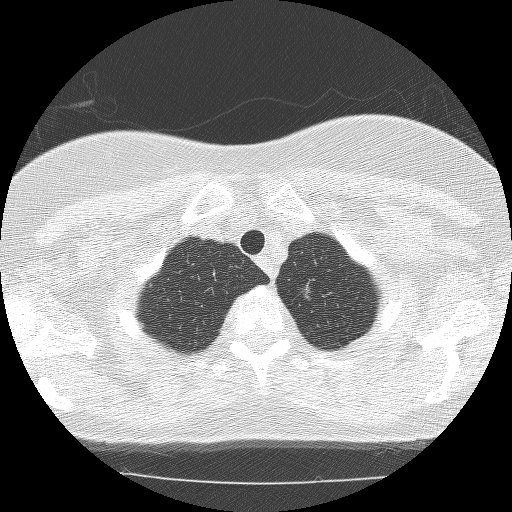
Chest CT (low-dose screening protocol), one axial image, second annual screen, lung window (W 1500 / L -600 HU), 512 × 512 image matrix, field of view 310 × 310 mm. Female participant, aged 59 years at enrolment. Former smoker at enrolment.
- Expert reader's lesion annotation, box from (x=277, y=273) to (x=326, y=316) px.
- The screening reader recorded 3 non-calcified nodules or masses ≥4 mm on this exam (right upper lobe, left upper lobe, right upper lobe); which of them this box marks is not recorded.
- Official screen result: positive, other.